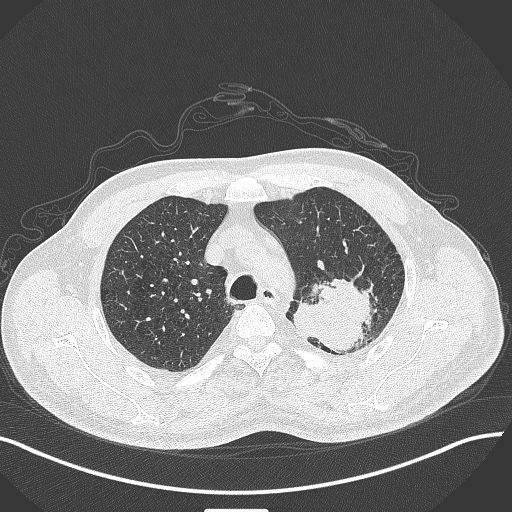
Chest CT, one axial slice. Position 329 of 429 along the scan axis. Reconstruction kernel B70f. 120 kVp. Lung window (W 1500 / L -600 HU). 1 mm slice thickness. 512 × 512 image matrix. Male patient, age 55 years. From the clinical record (not read from this slice): clinical TNM (as recorded): T3 N0 M1c; histopathological grade: G3.
Outlined on this slice (rectangle marked by the reading radiologist):
- lung tumour (recorded histology: adenocarcinoma): bounding box [x1, y1, x2, y2] px = [295, 279, 380, 356]